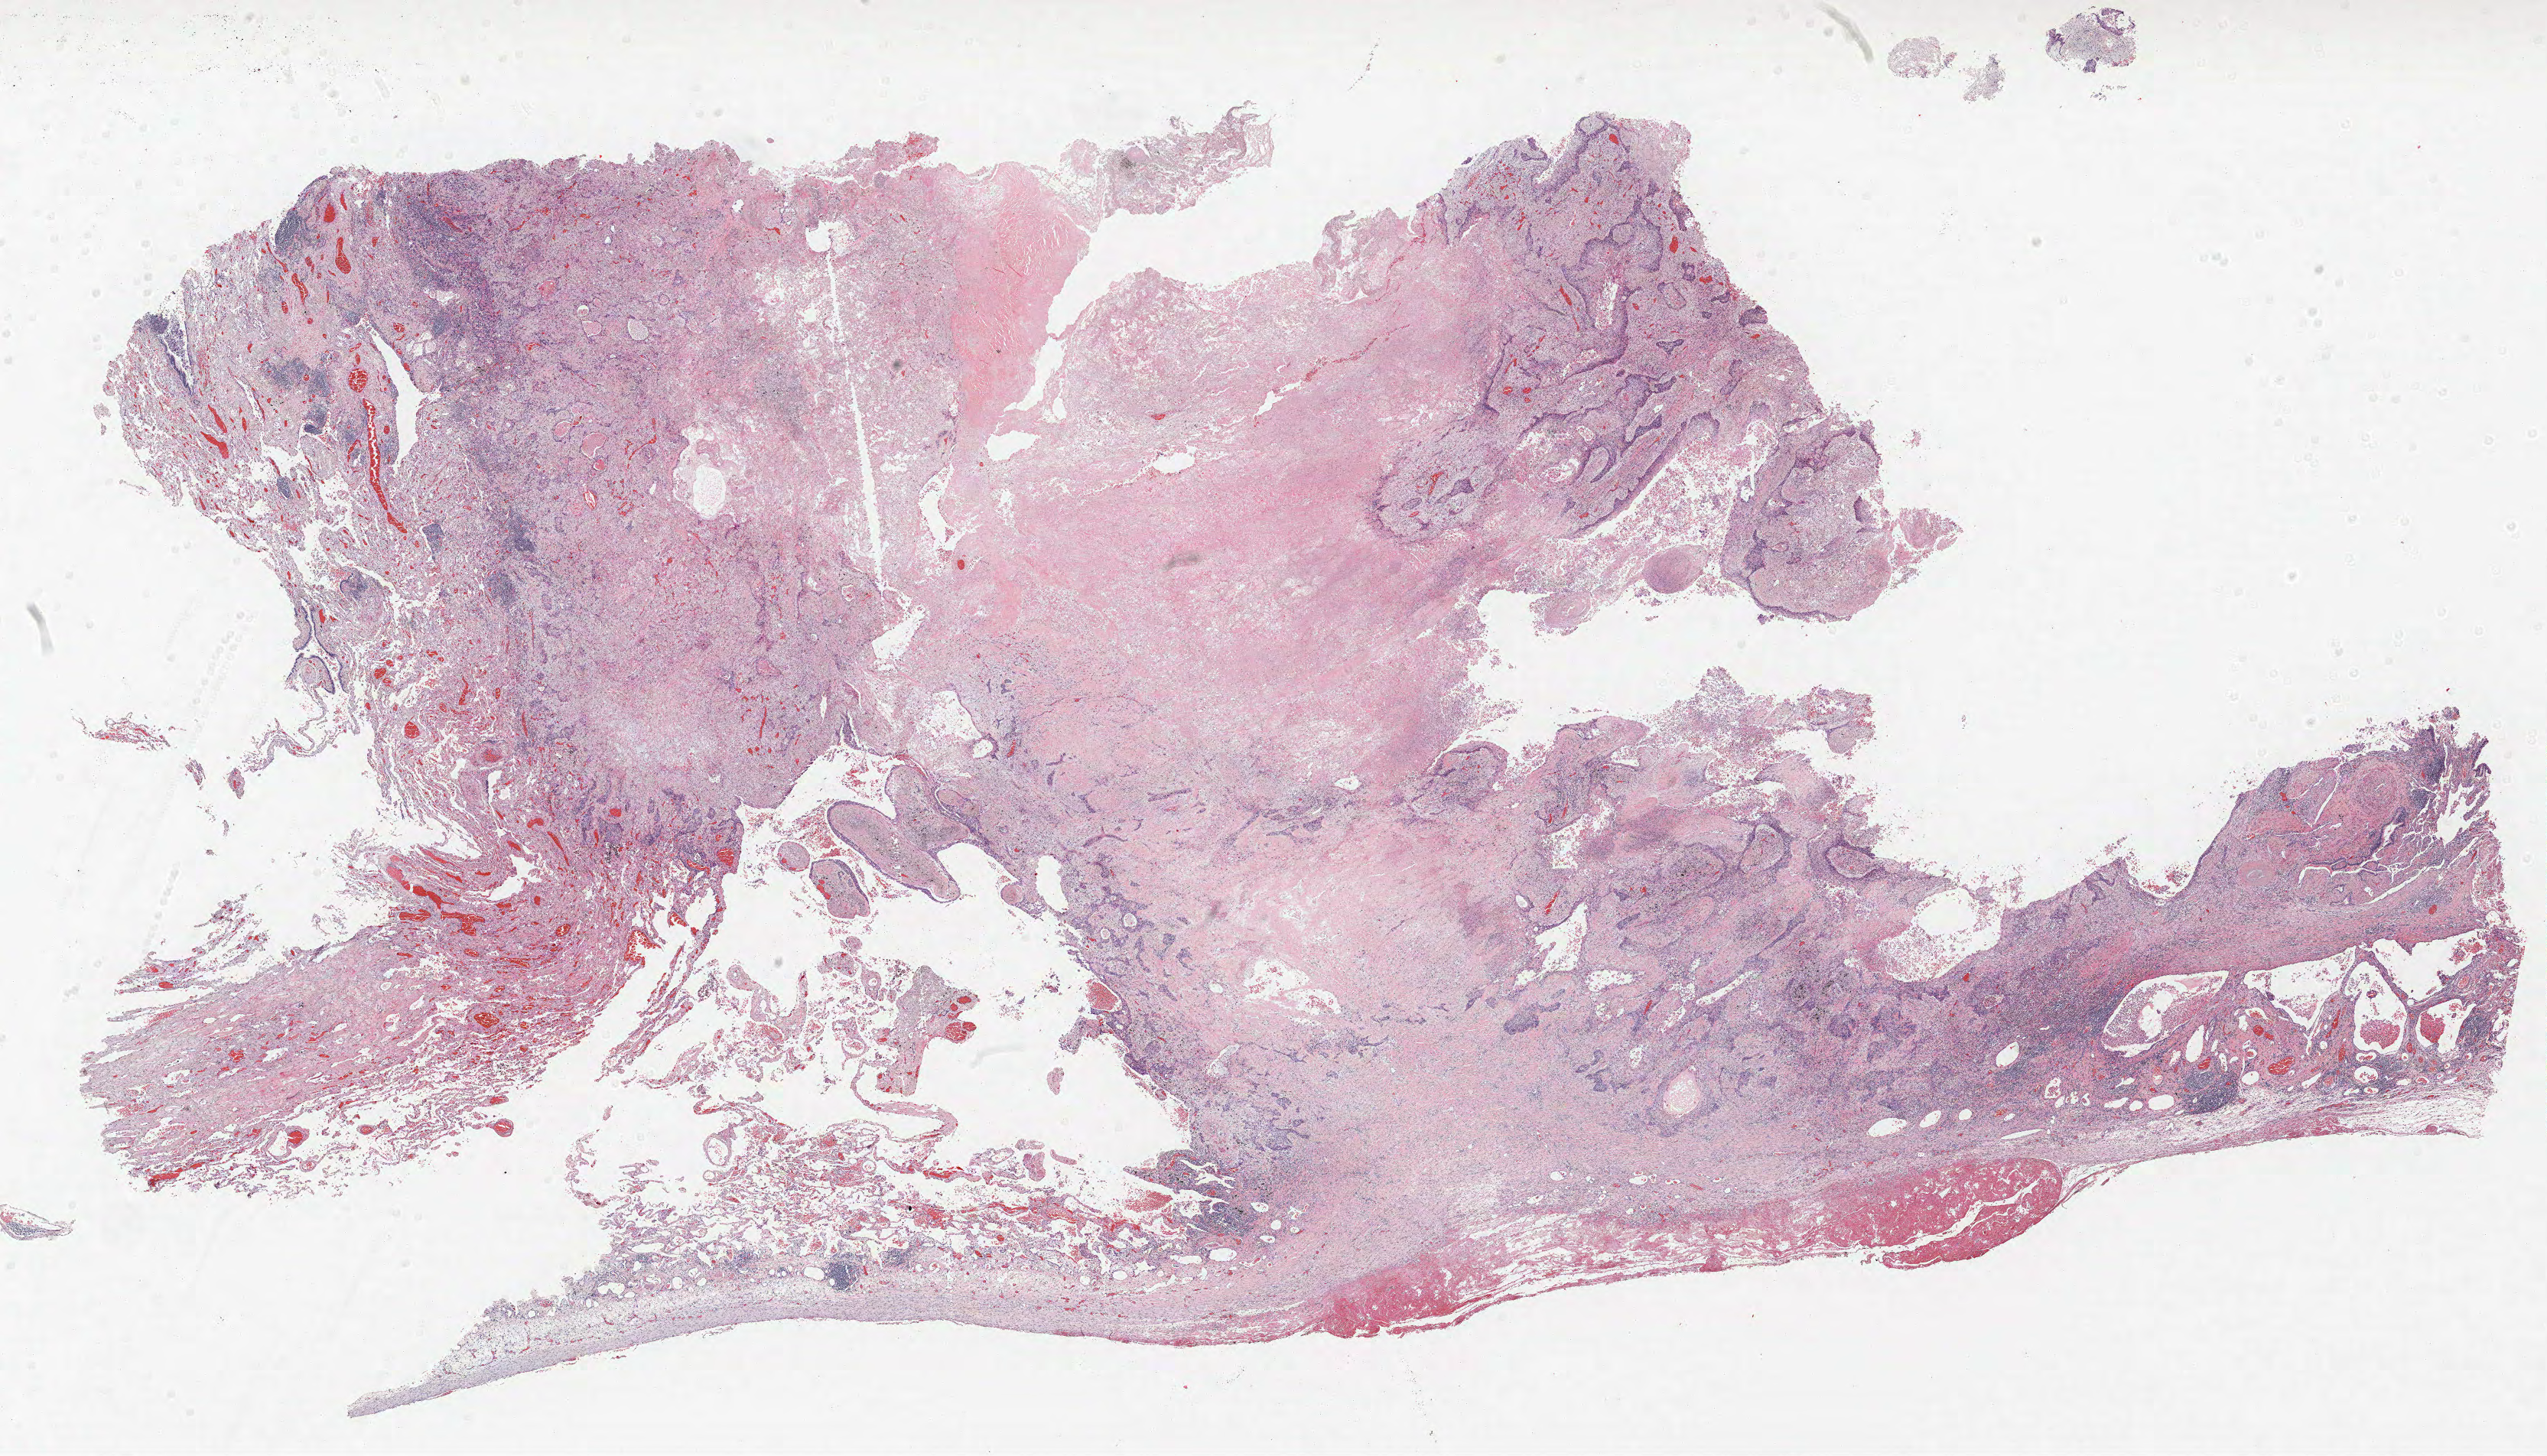
Whole-slide histology image, Hematoxylin and eosin (H&E) stained — whole scanned area (about 26.6 x 15.2 mm, acquisition: 40x scan) shown as a low-resolution overview, formalin-fixed paraffin-embedded (FFPE) section, lung tissue. Male patient, aged 59 at enrolment. Grade: moderately differentiated (G2).
Stage (AJCC 6th edition): IA. Participant's lung-cancer diagnosis: Squamous cell carcinoma, NOS. Tumour size (pathology): 30 mm. Primary tumour location (clinical record): right upper lobe.